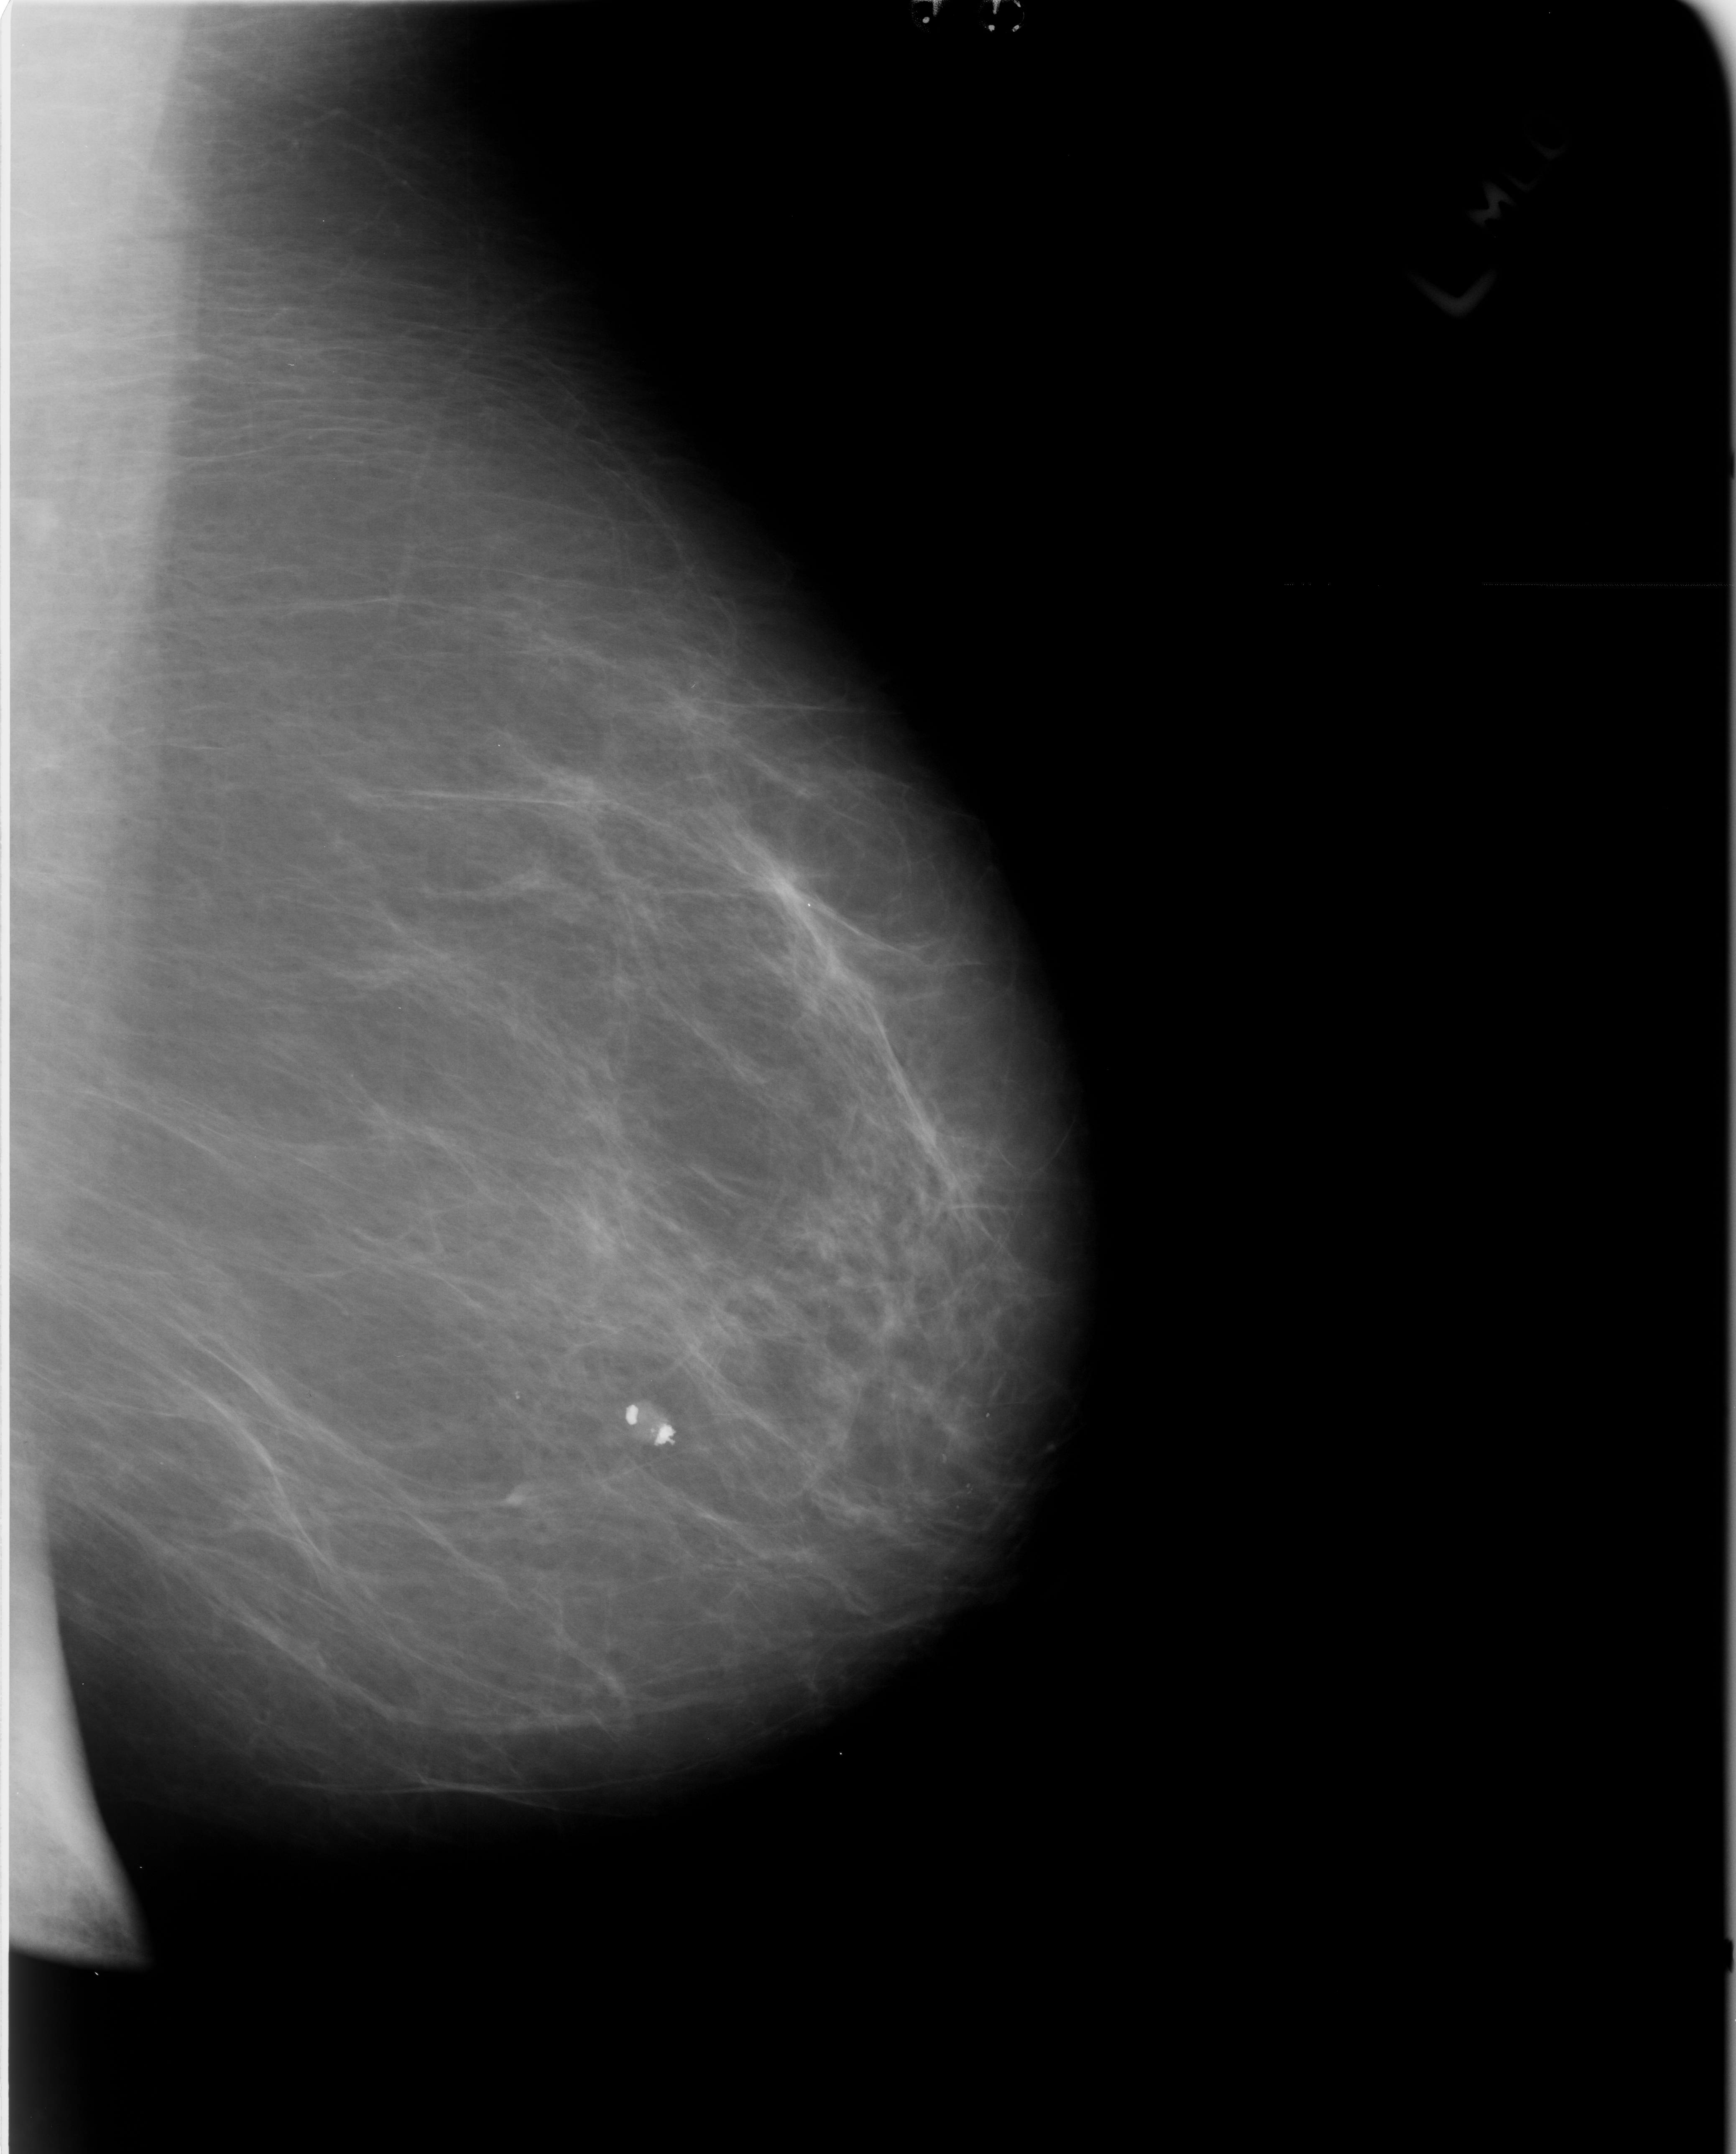
Scanned film-screen mammogram, left breast, MLO view, BI-RADS breast density category 1 (scale 1–4).
Finding: calcifications, morphology coarse; BI-RADS assessment category 2; benign; no additional work-up was recommended (benign without callback).